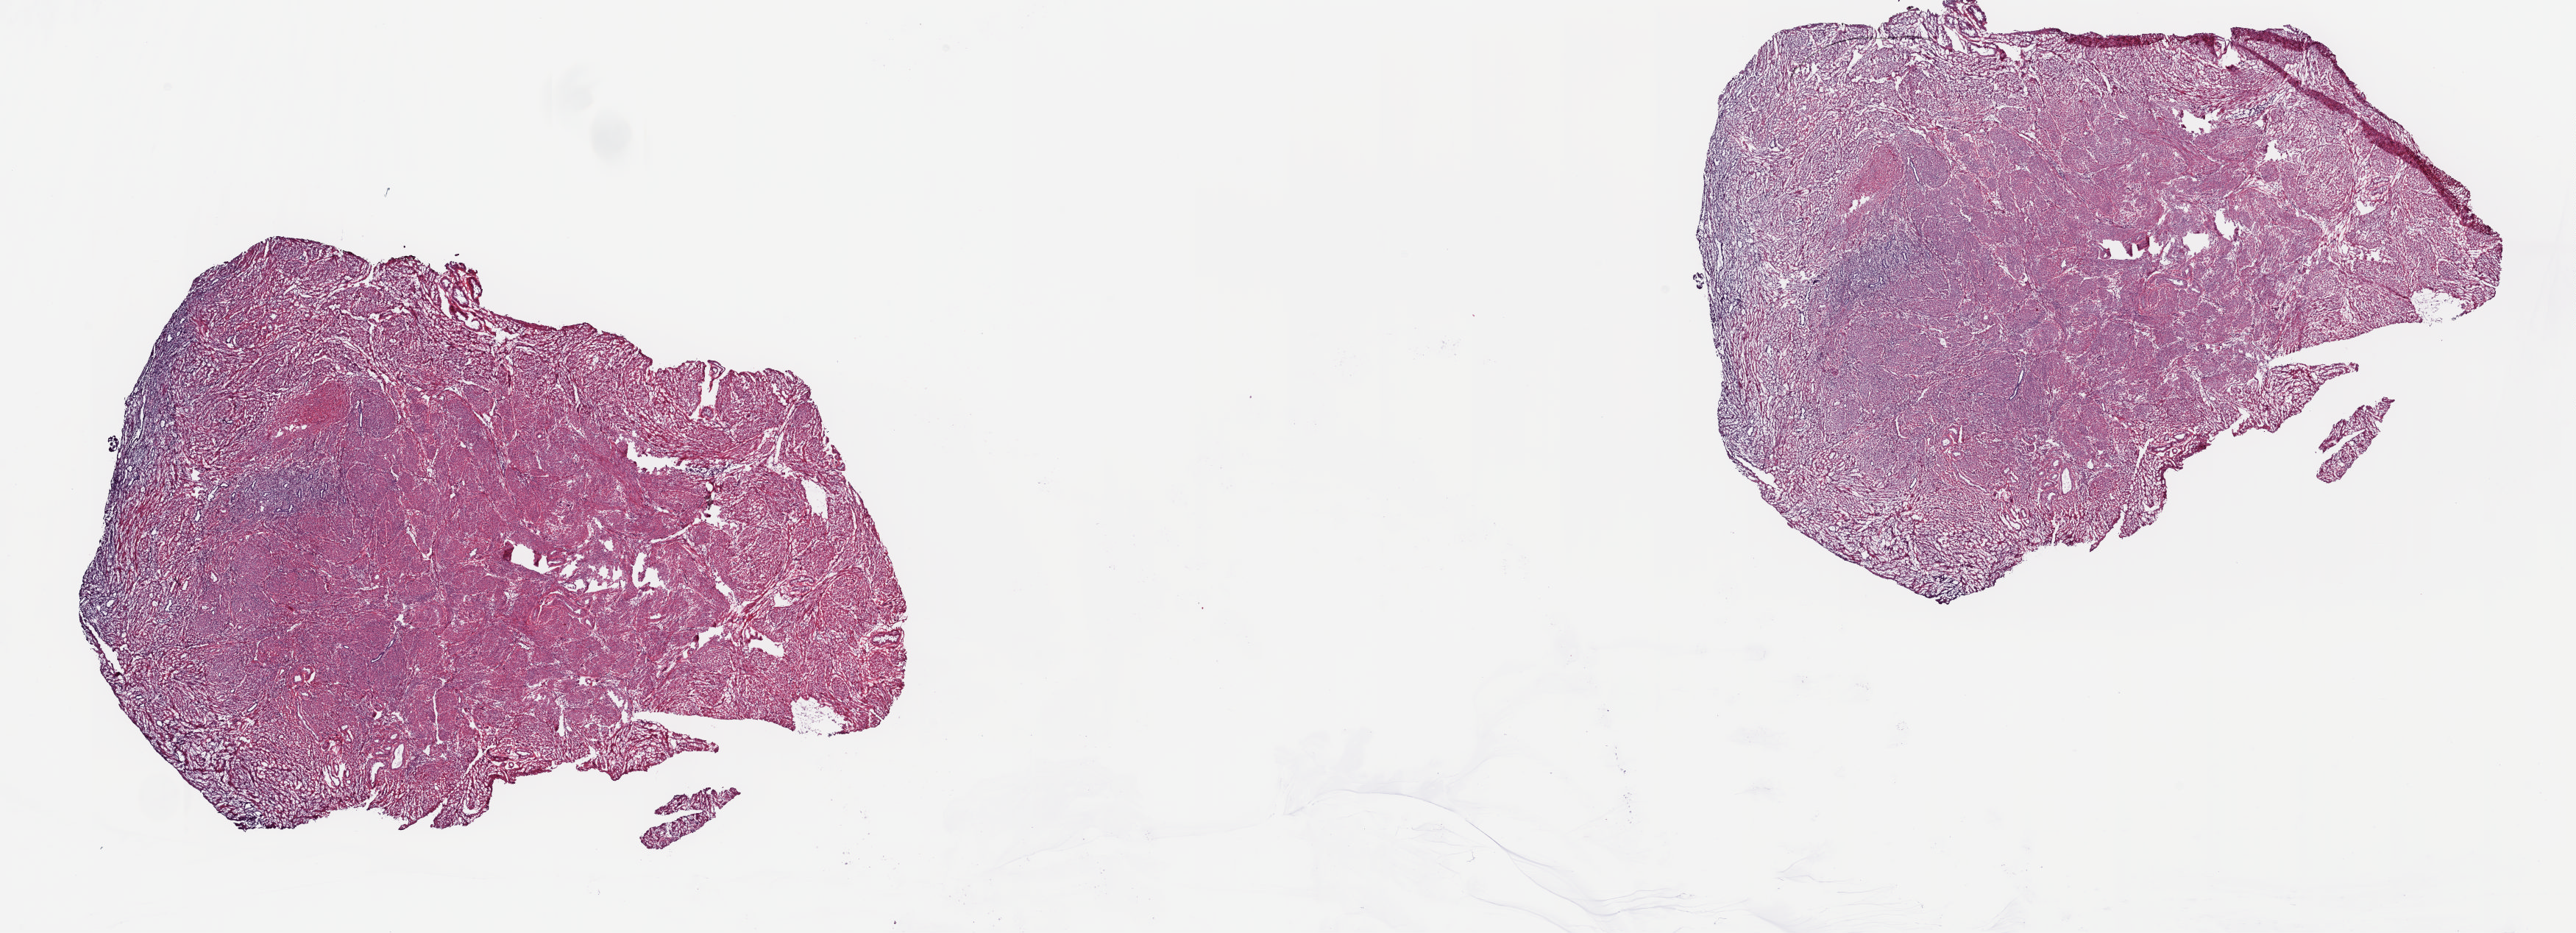
Whole-slide histology image, H&E-stained, low-resolution overview of the scanned area, about 27.8 x 10.1 mm (from a 20x scan); frozen section from the top of the tissue portion; sample: solid tissue normal (non-tumour tissue), uterus. Patient: female, age at initial diagnosis 46 years. Composition of this section per pathologist review: tumour cells 0%, tumour nuclei 0%, normal cells 100%, stromal cells 0%, necrosis 0%. Inflammatory infiltration, as recorded: lymphocyte infiltration 1%, monocyte infiltration 0%, neutrophil infiltration 0%.
* this section: solid tissue normal sample (biorepository sample class)
* patient diagnosis: Endometrioid adenocarcinoma, NOS